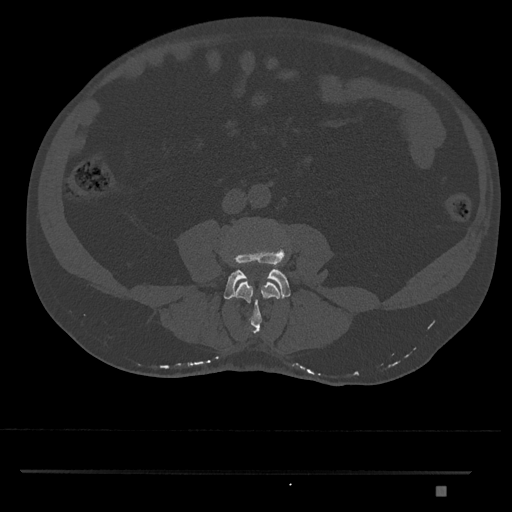
CT including the spine, one axial slice; position 646 of 1134 along the scan axis; reconstruction kernel Br40s/3; 120 kVp; bone window (W 1800 / L 400 HU); 512 × 512 image matrix, field of view 429 × 429 mm. Male patient, age 65 years. Case-level facts recorded for this patient, not image findings: primary cancer: prostate.
Structures marked on this image (semi-automatically segmented with operator editing):
- L3 vertebra: box from (x=234, y=281) to (x=280, y=334) px
- L4 vertebra: (x=224, y=243)–(x=291, y=300)